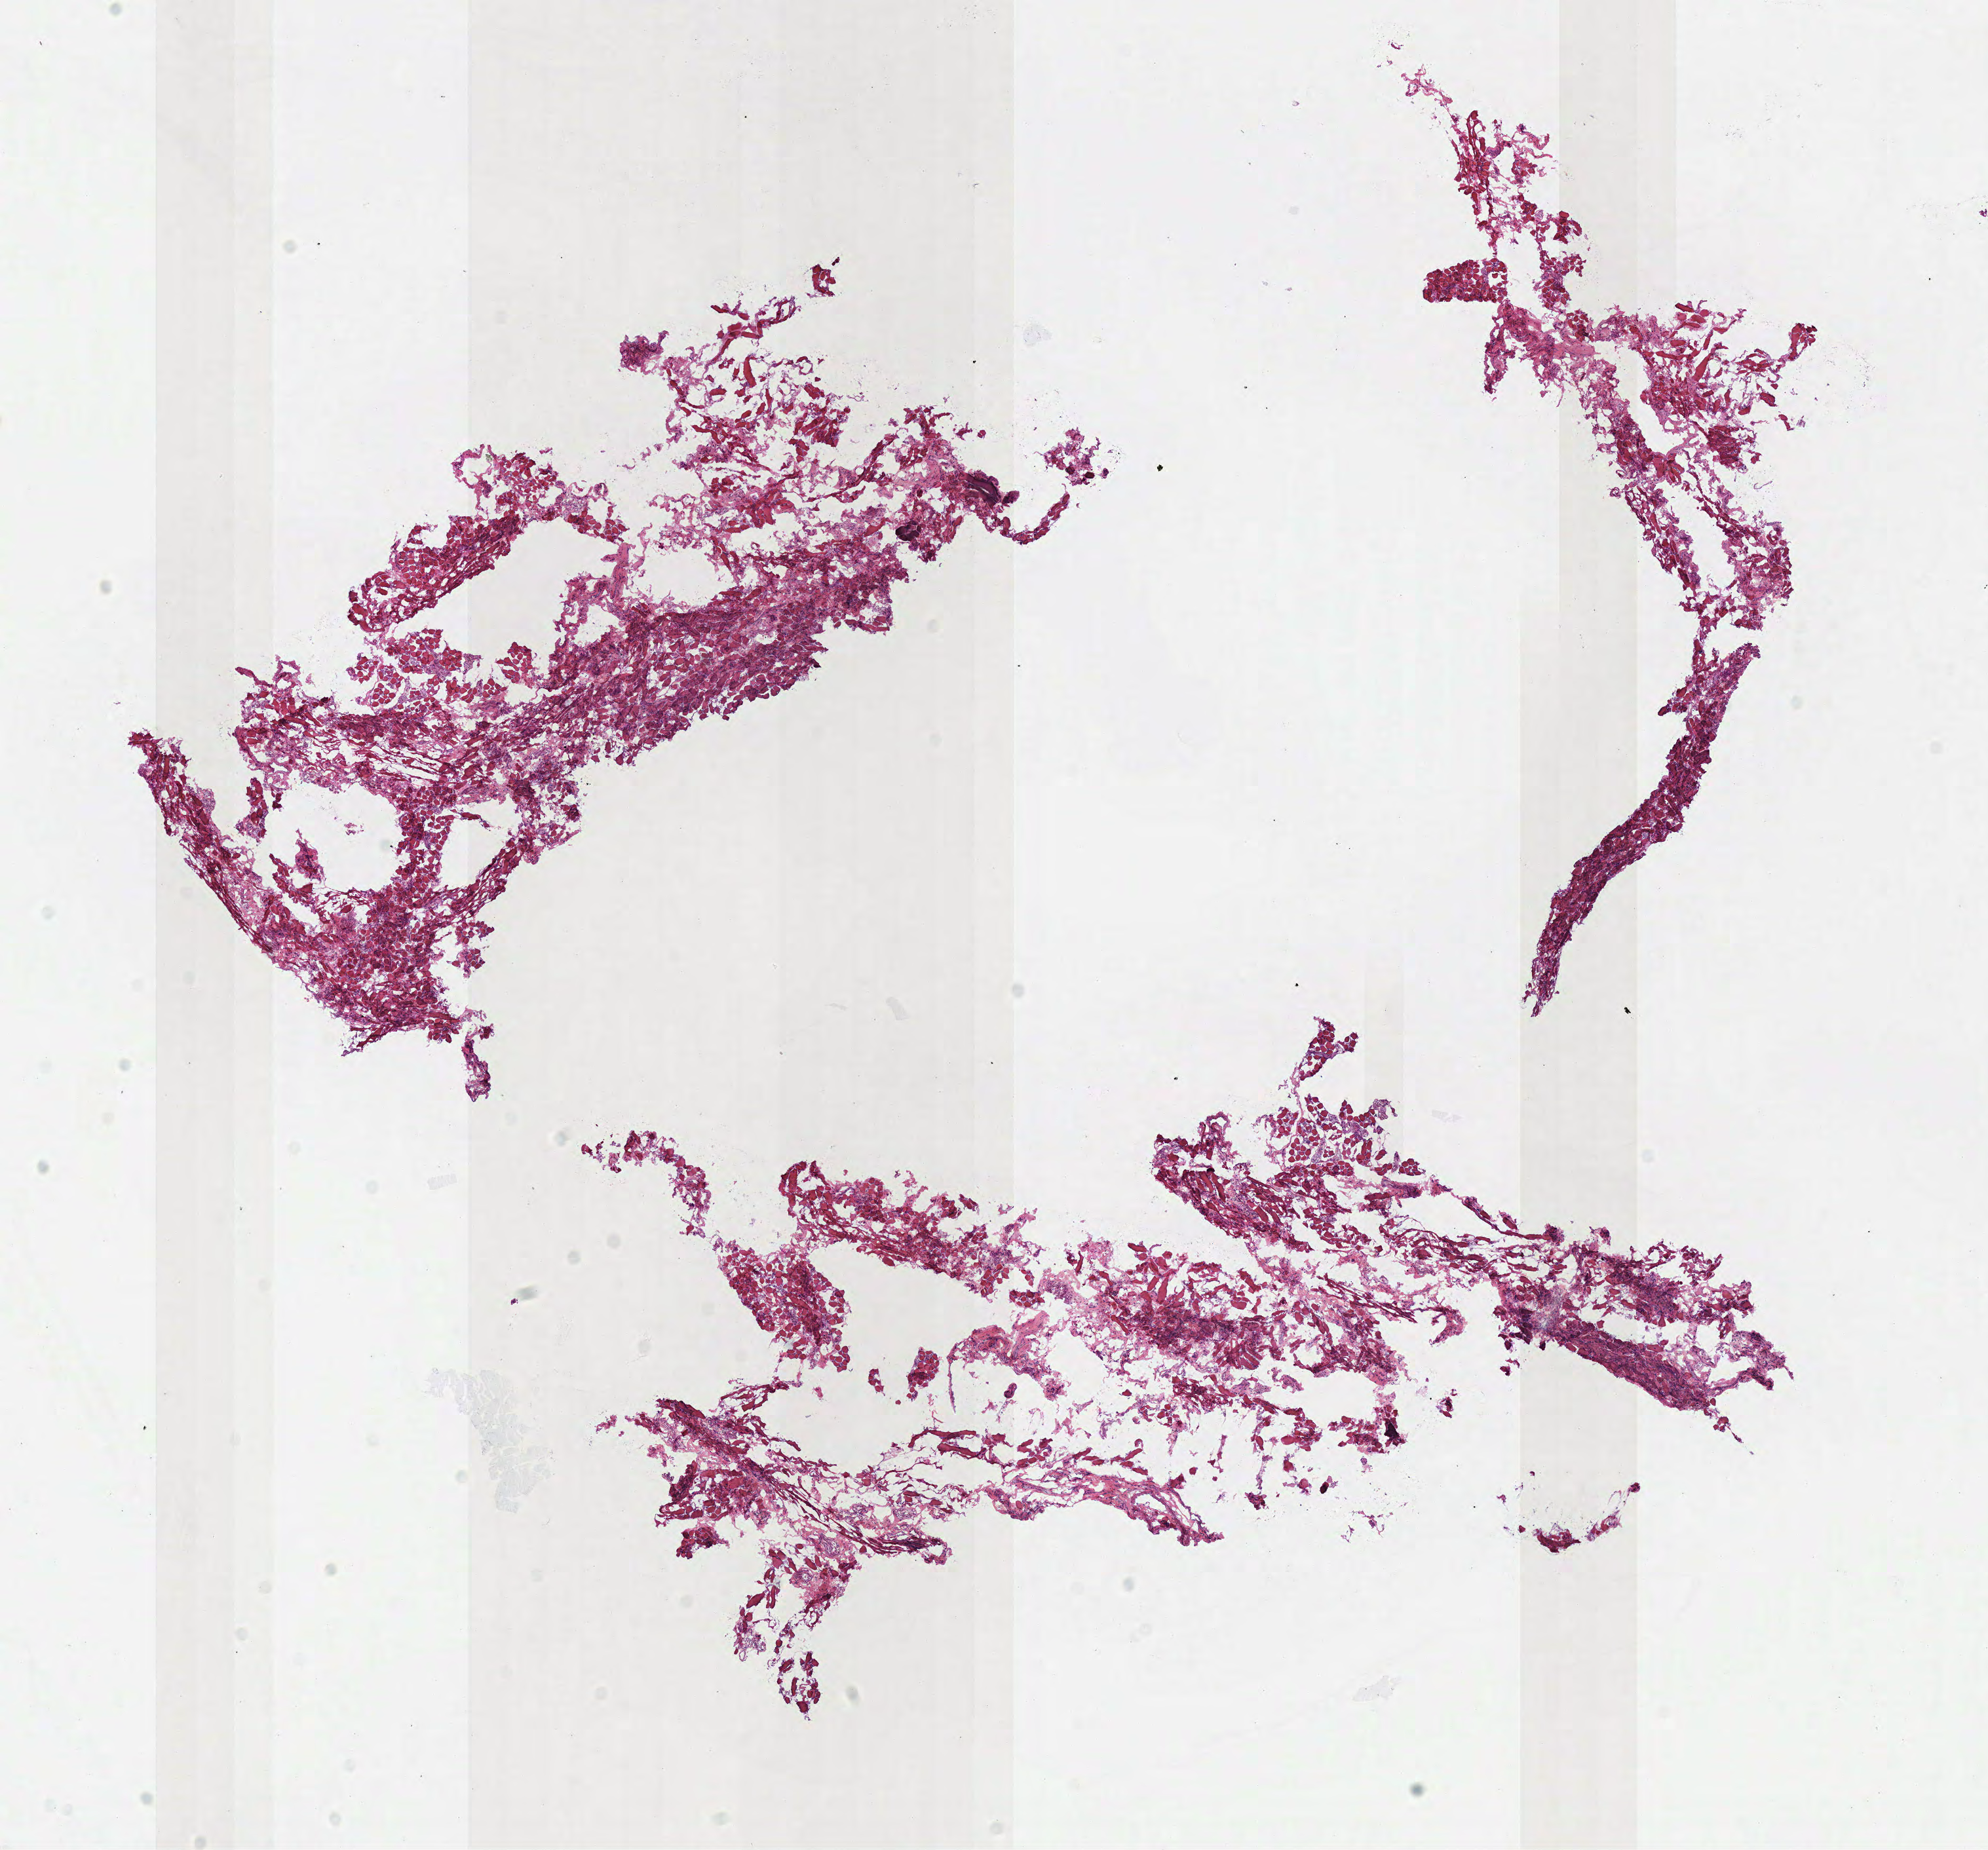
Whole-slide histology image, Hematoxylin and eosin (H&E) stained, shown as a low-resolution overview of the whole scanned area (about 12.0 x 11.1 mm, acquisition: 40x scan), frozen section, solid tissue normal (non-tumour tissue) sample from the head and neck. Male, age 60 years at initial diagnosis.
This section: solid tissue normal sample (biorepository sample class). Patient diagnosis: Squamous cell carcinoma, NOS (tongue, NOS).